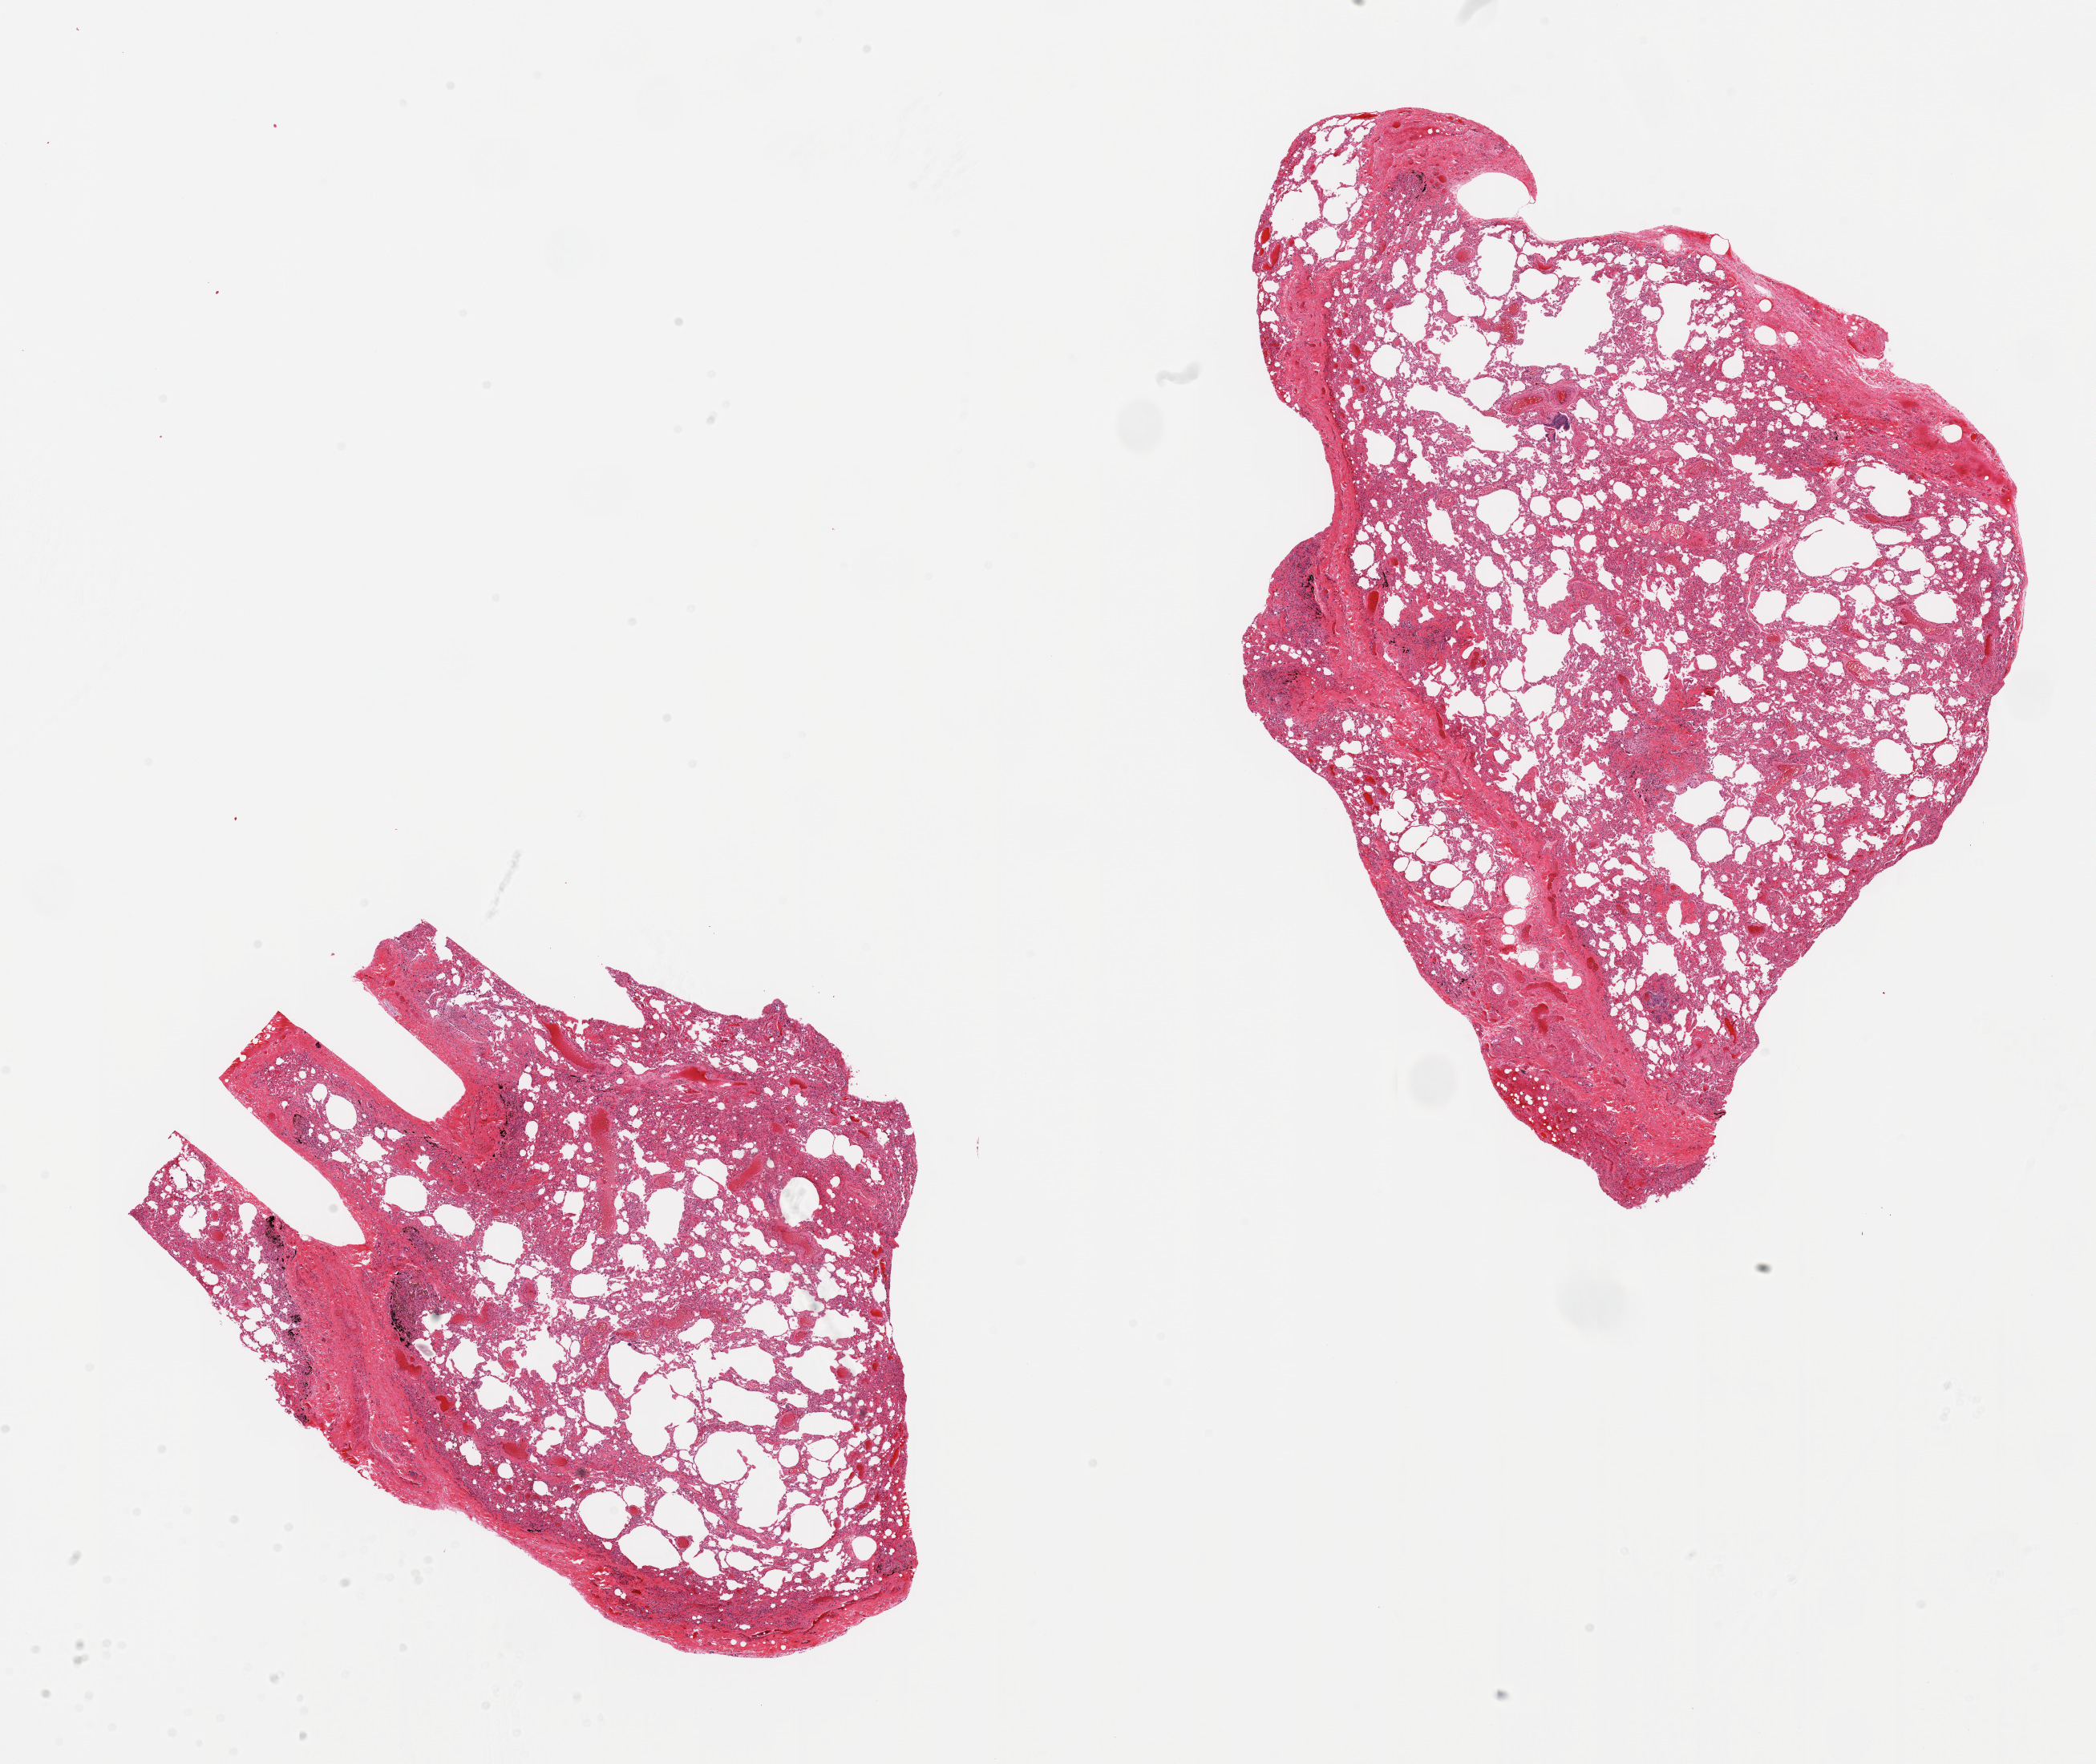
Digitized H&E-stained section, brightfield — low-resolution overview of the scanned area, about 20.7 x 17.4 mm; PAXgene-fixed paraffin-embedded (PFPE) section; sampled site (target tissue): lung; donor tissue sample.
Review note (as recorded): 2 pieces, moderate congestion, marked patchy interstitial fibrosis; emphysematous changes.